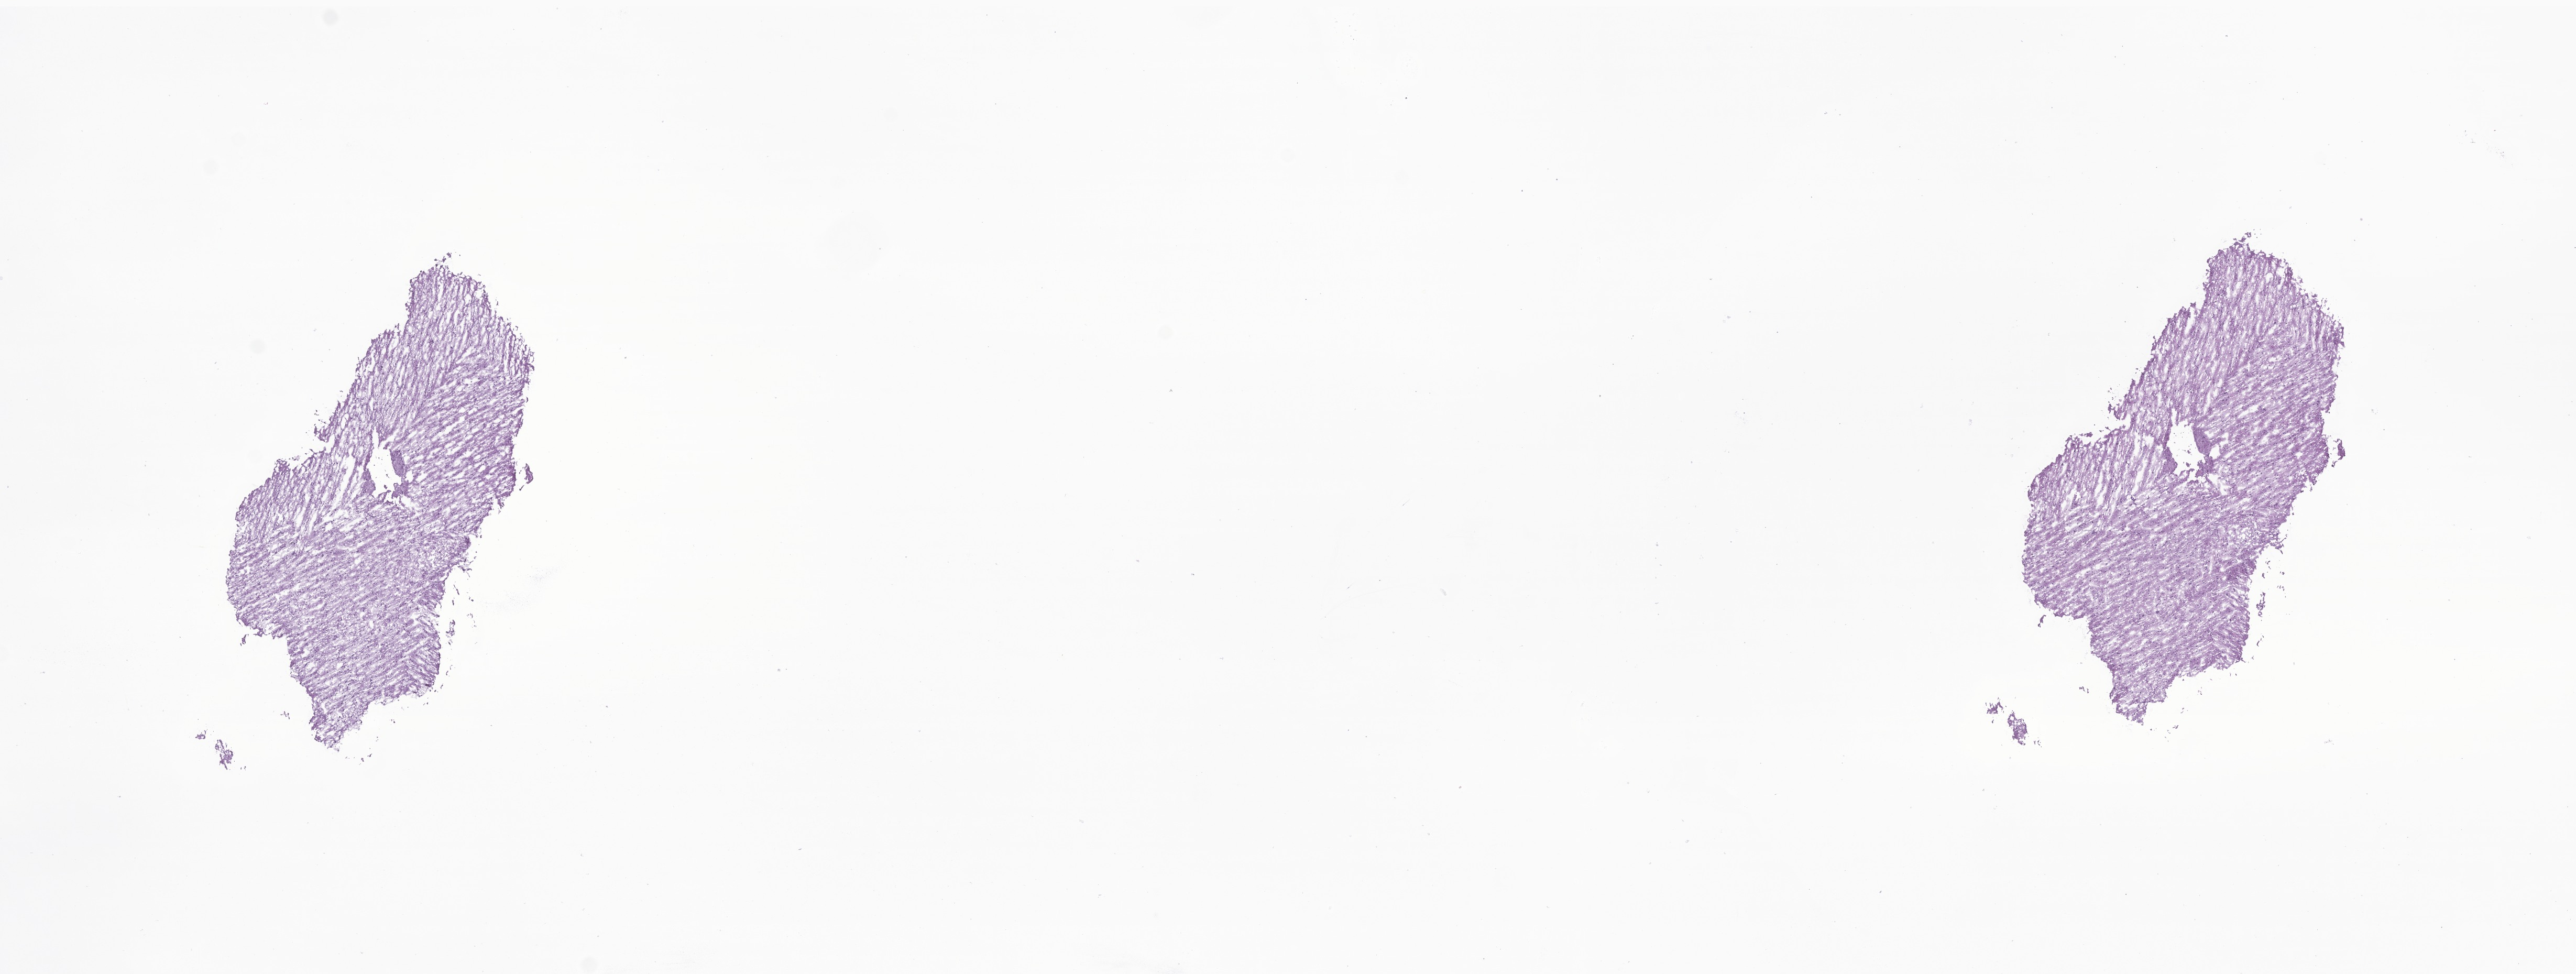
H&E whole-slide image of tumor tissue from the adrenal gland — low-resolution overview of the scanned area, about 20.7 x 7.8 mm, frozen section (OCT-embedded). Female patient, age 50 months.
Diagnosis: Adrenal cortical carcinoma.